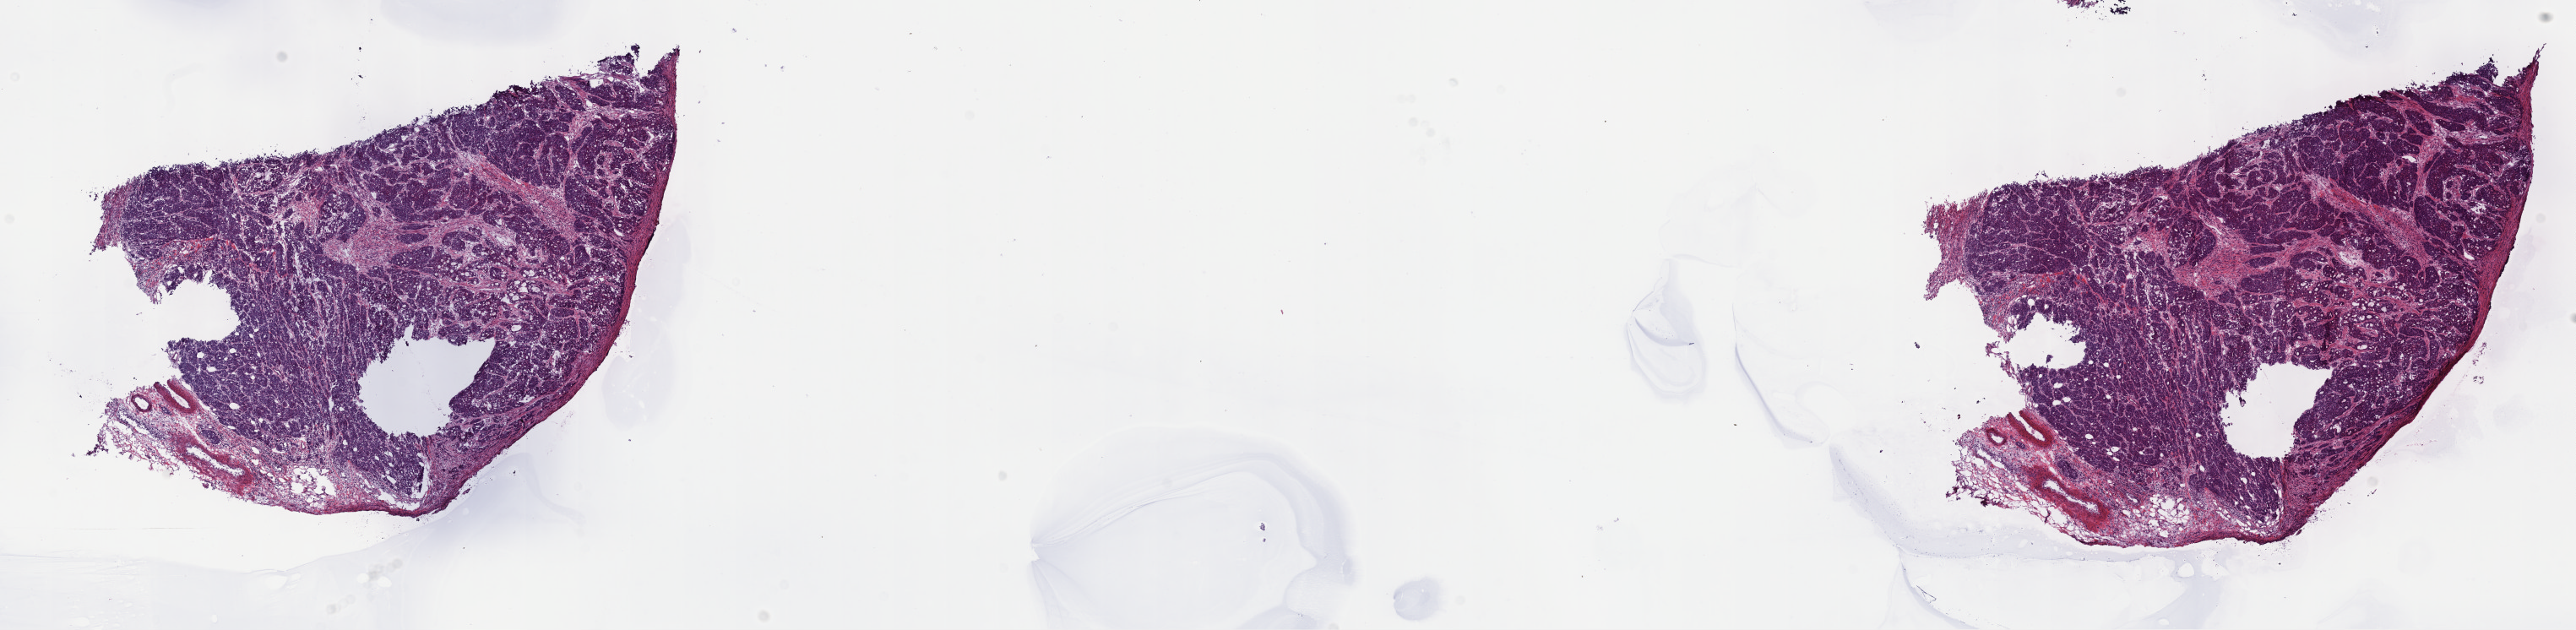
Digitized H&E-stained tissue section (whole slide), shown as a low-resolution overview of the whole scanned area (about 24.7 x 6.0 mm, from a 40x scan), frozen section, primary tumour sample from the colon. Patient: female, age at initial diagnosis 40 years. Composition of this section per pathologist review: tumour cells 80%, tumour nuclei 80%, normal cells 5%, stromal cells 15%, necrosis 0%. Infiltration values recorded for this section: lymphocyte infiltration 5%, monocyte infiltration 0%, neutrophil infiltration 0%.
Pathologic diagnosis: Adenocarcinoma, NOS (ascending colon). TNM: T4a N2b M1a. AJCC pathologic stage: IV (6th edition).